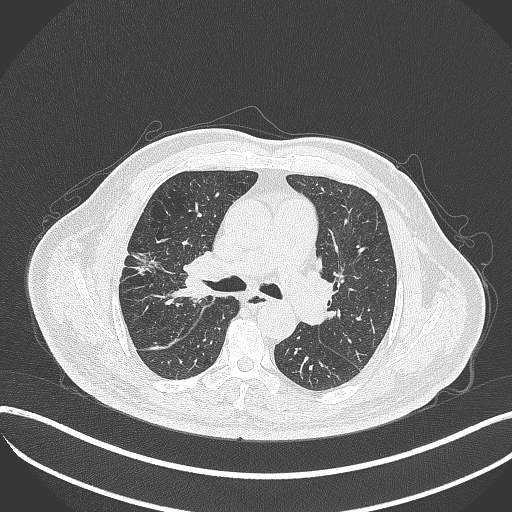
Chest CT, one axial slice; slice 222 of 401 in the series (ordered by position); reconstruction kernel B70f; 120 kVp; lung window (W 1500 / L -600 HU); 1 mm slice thickness; 512 × 512 image matrix, field of view 400 × 400 mm. Patient: male, 72 years. Case-level facts recorded for this patient, not image findings: clinical TNM (as recorded): T1c N0 M0.
Outlined on this slice (bounding box drawn by a radiologist):
- lung tumour (recorded histology: squamous cell carcinoma): bounding box <164,261,203,308> (left, top, right, bottom; pixels)